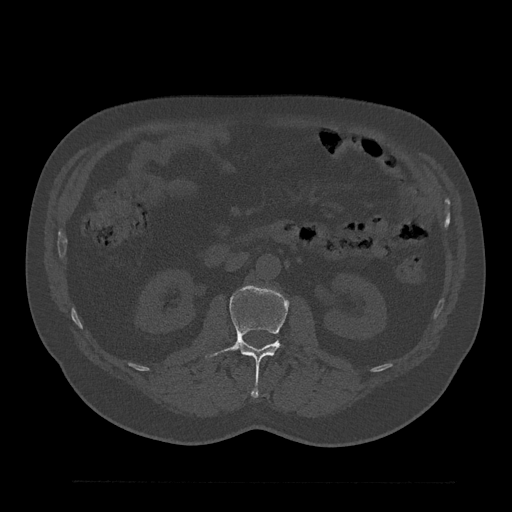
CT including the spine, one axial slice; slice 96 of 797 in the series (ordered by position); reconstruction kernel Br40s/3; 120 kVp; bone window (W 1800 / L 400 HU); 0.5 mm slice thickness; 512 × 512 image matrix. Patient: male, 61 years. From the clinical record (not read from this slice): primary cancer: prostate.
Outlined on this slice (semi-automatically segmented with operator editing):
- L2 vertebra: bounding box [x1, y1, x2, y2] px = [205, 285, 314, 397]